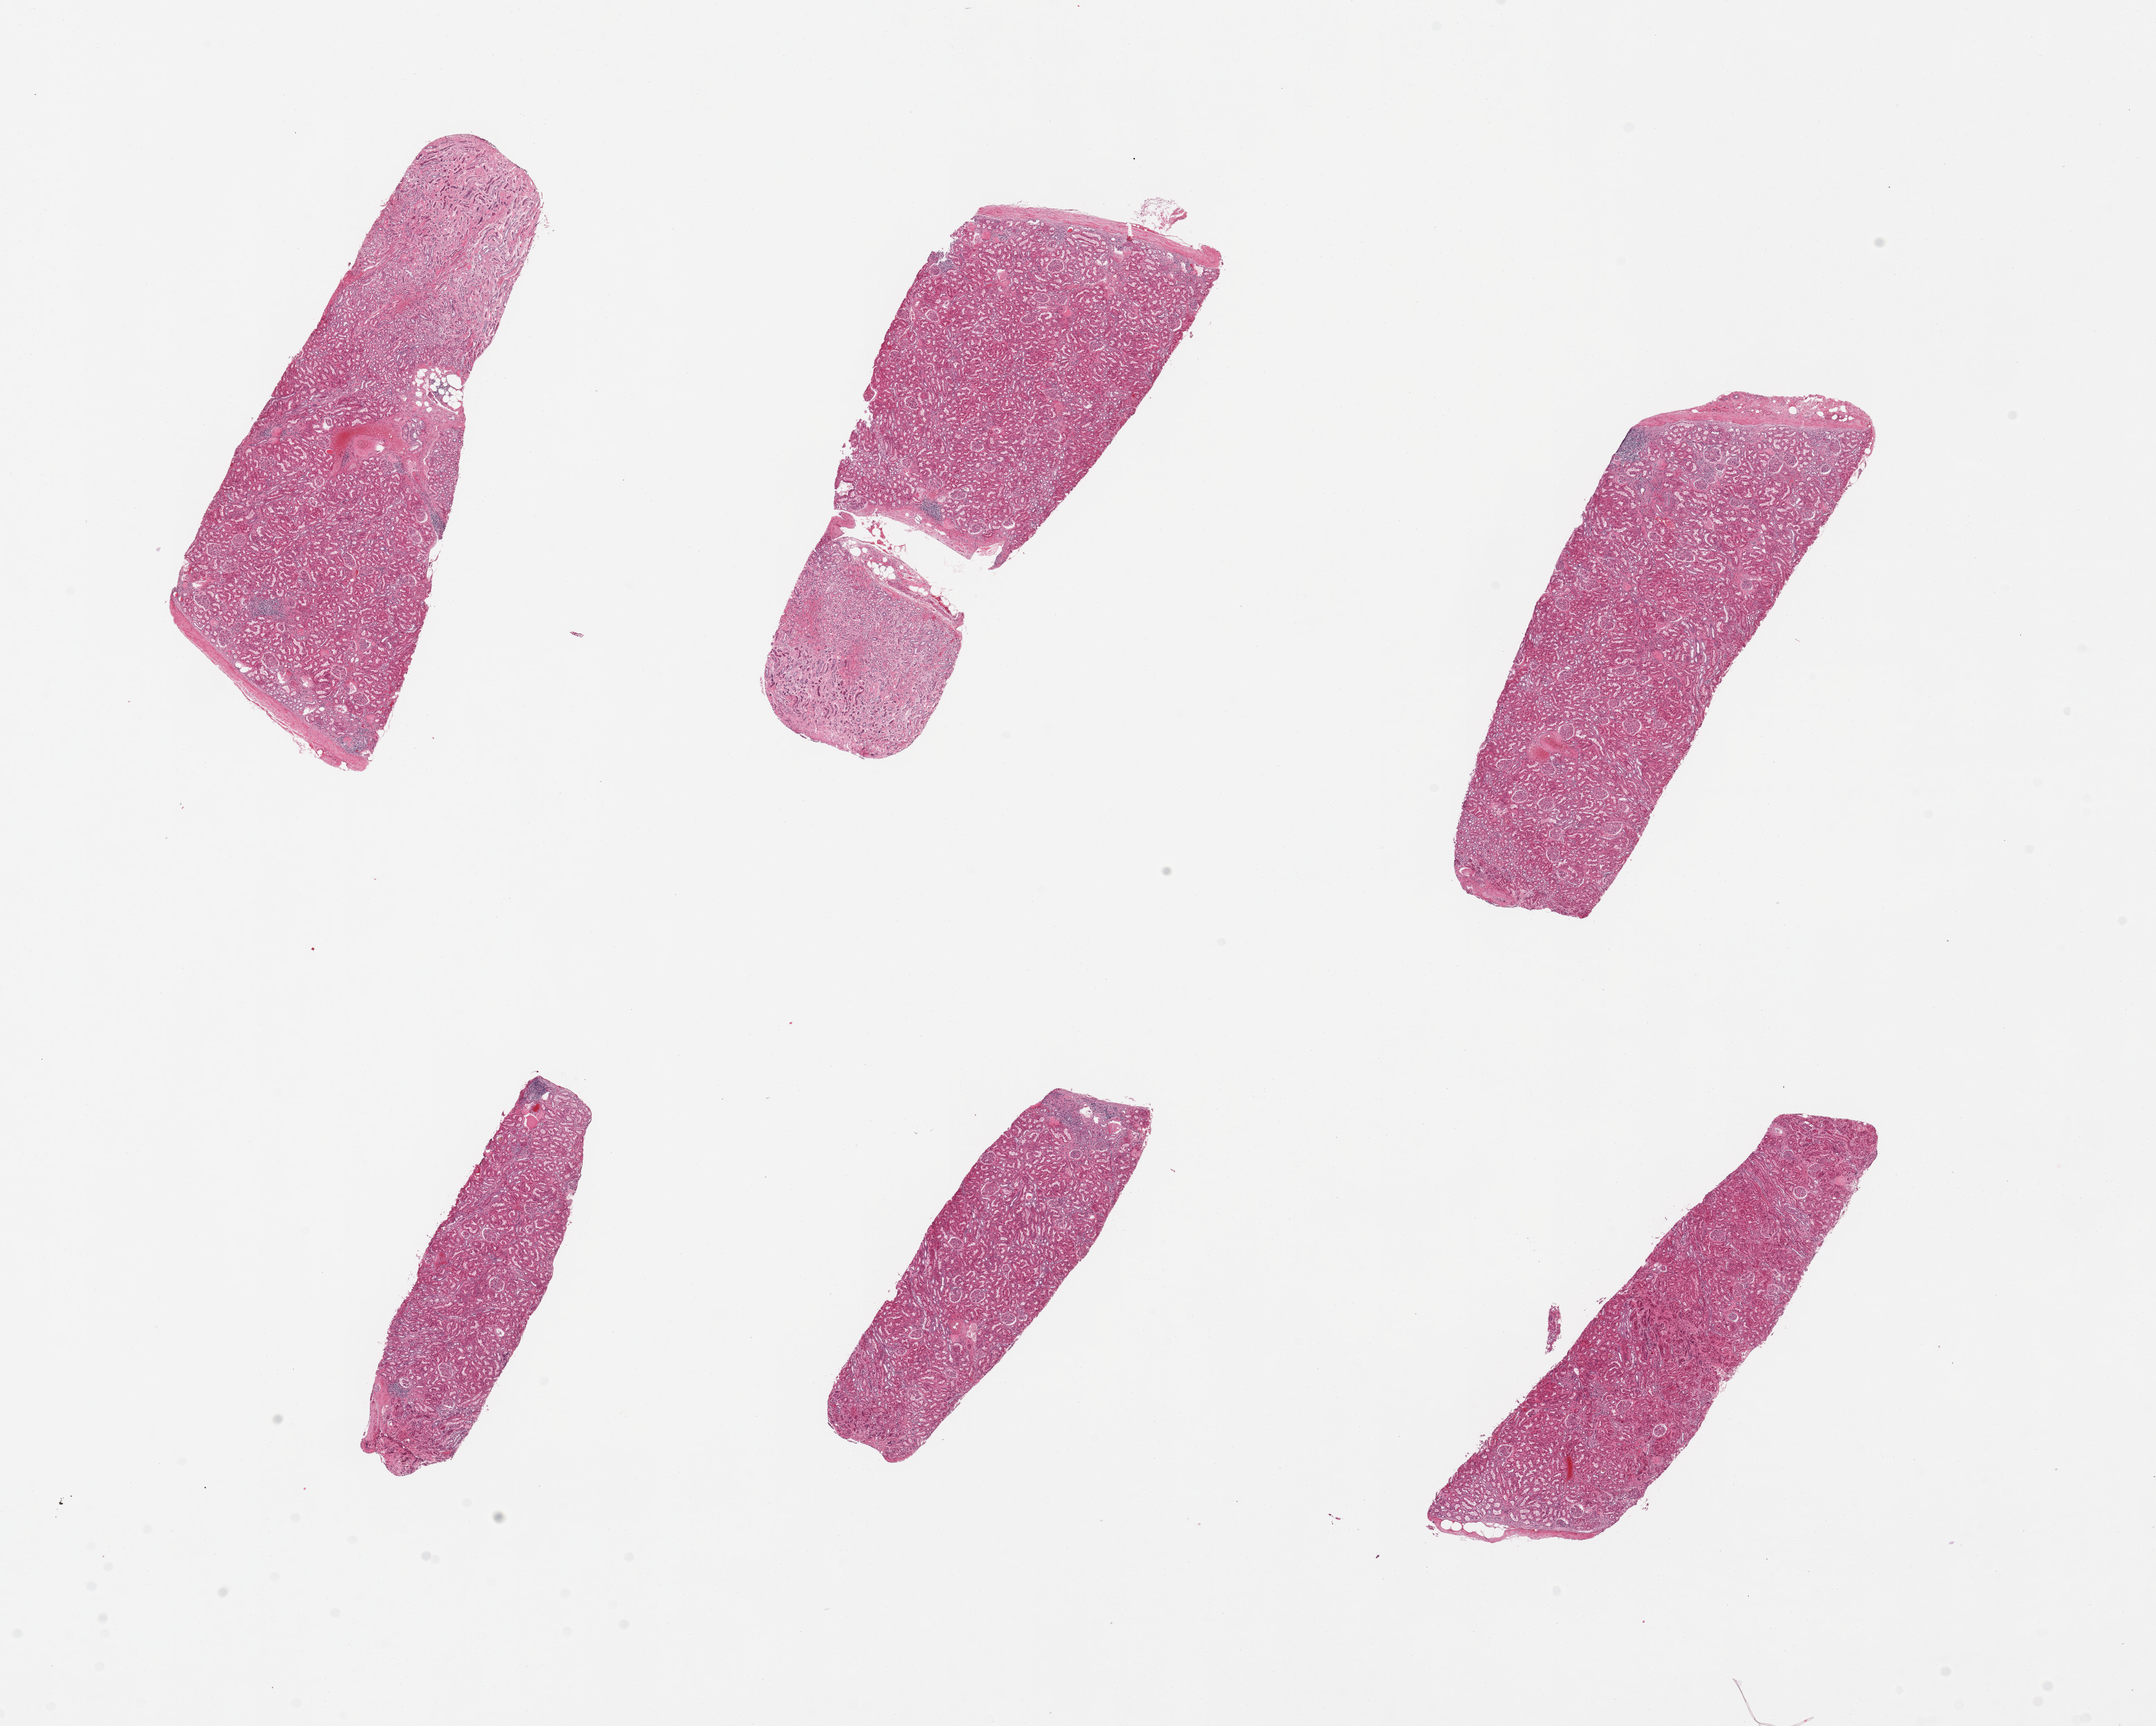
Haematoxylin and eosin whole-slide image, a low-resolution overview of the entire scanned area, about 24.6 x 19.7 mm (acquisition: 20x scan). PAXgene-fixed, paraffin-embedded tissue. Section of renal cortex (target tissue). Donor tissue sample. Female donor.
Review note (as recorded): 6 pieces, up to 7x3mm; glomeruli seen; patchy chronic interstitial nephritis; lymphoid aggregates.